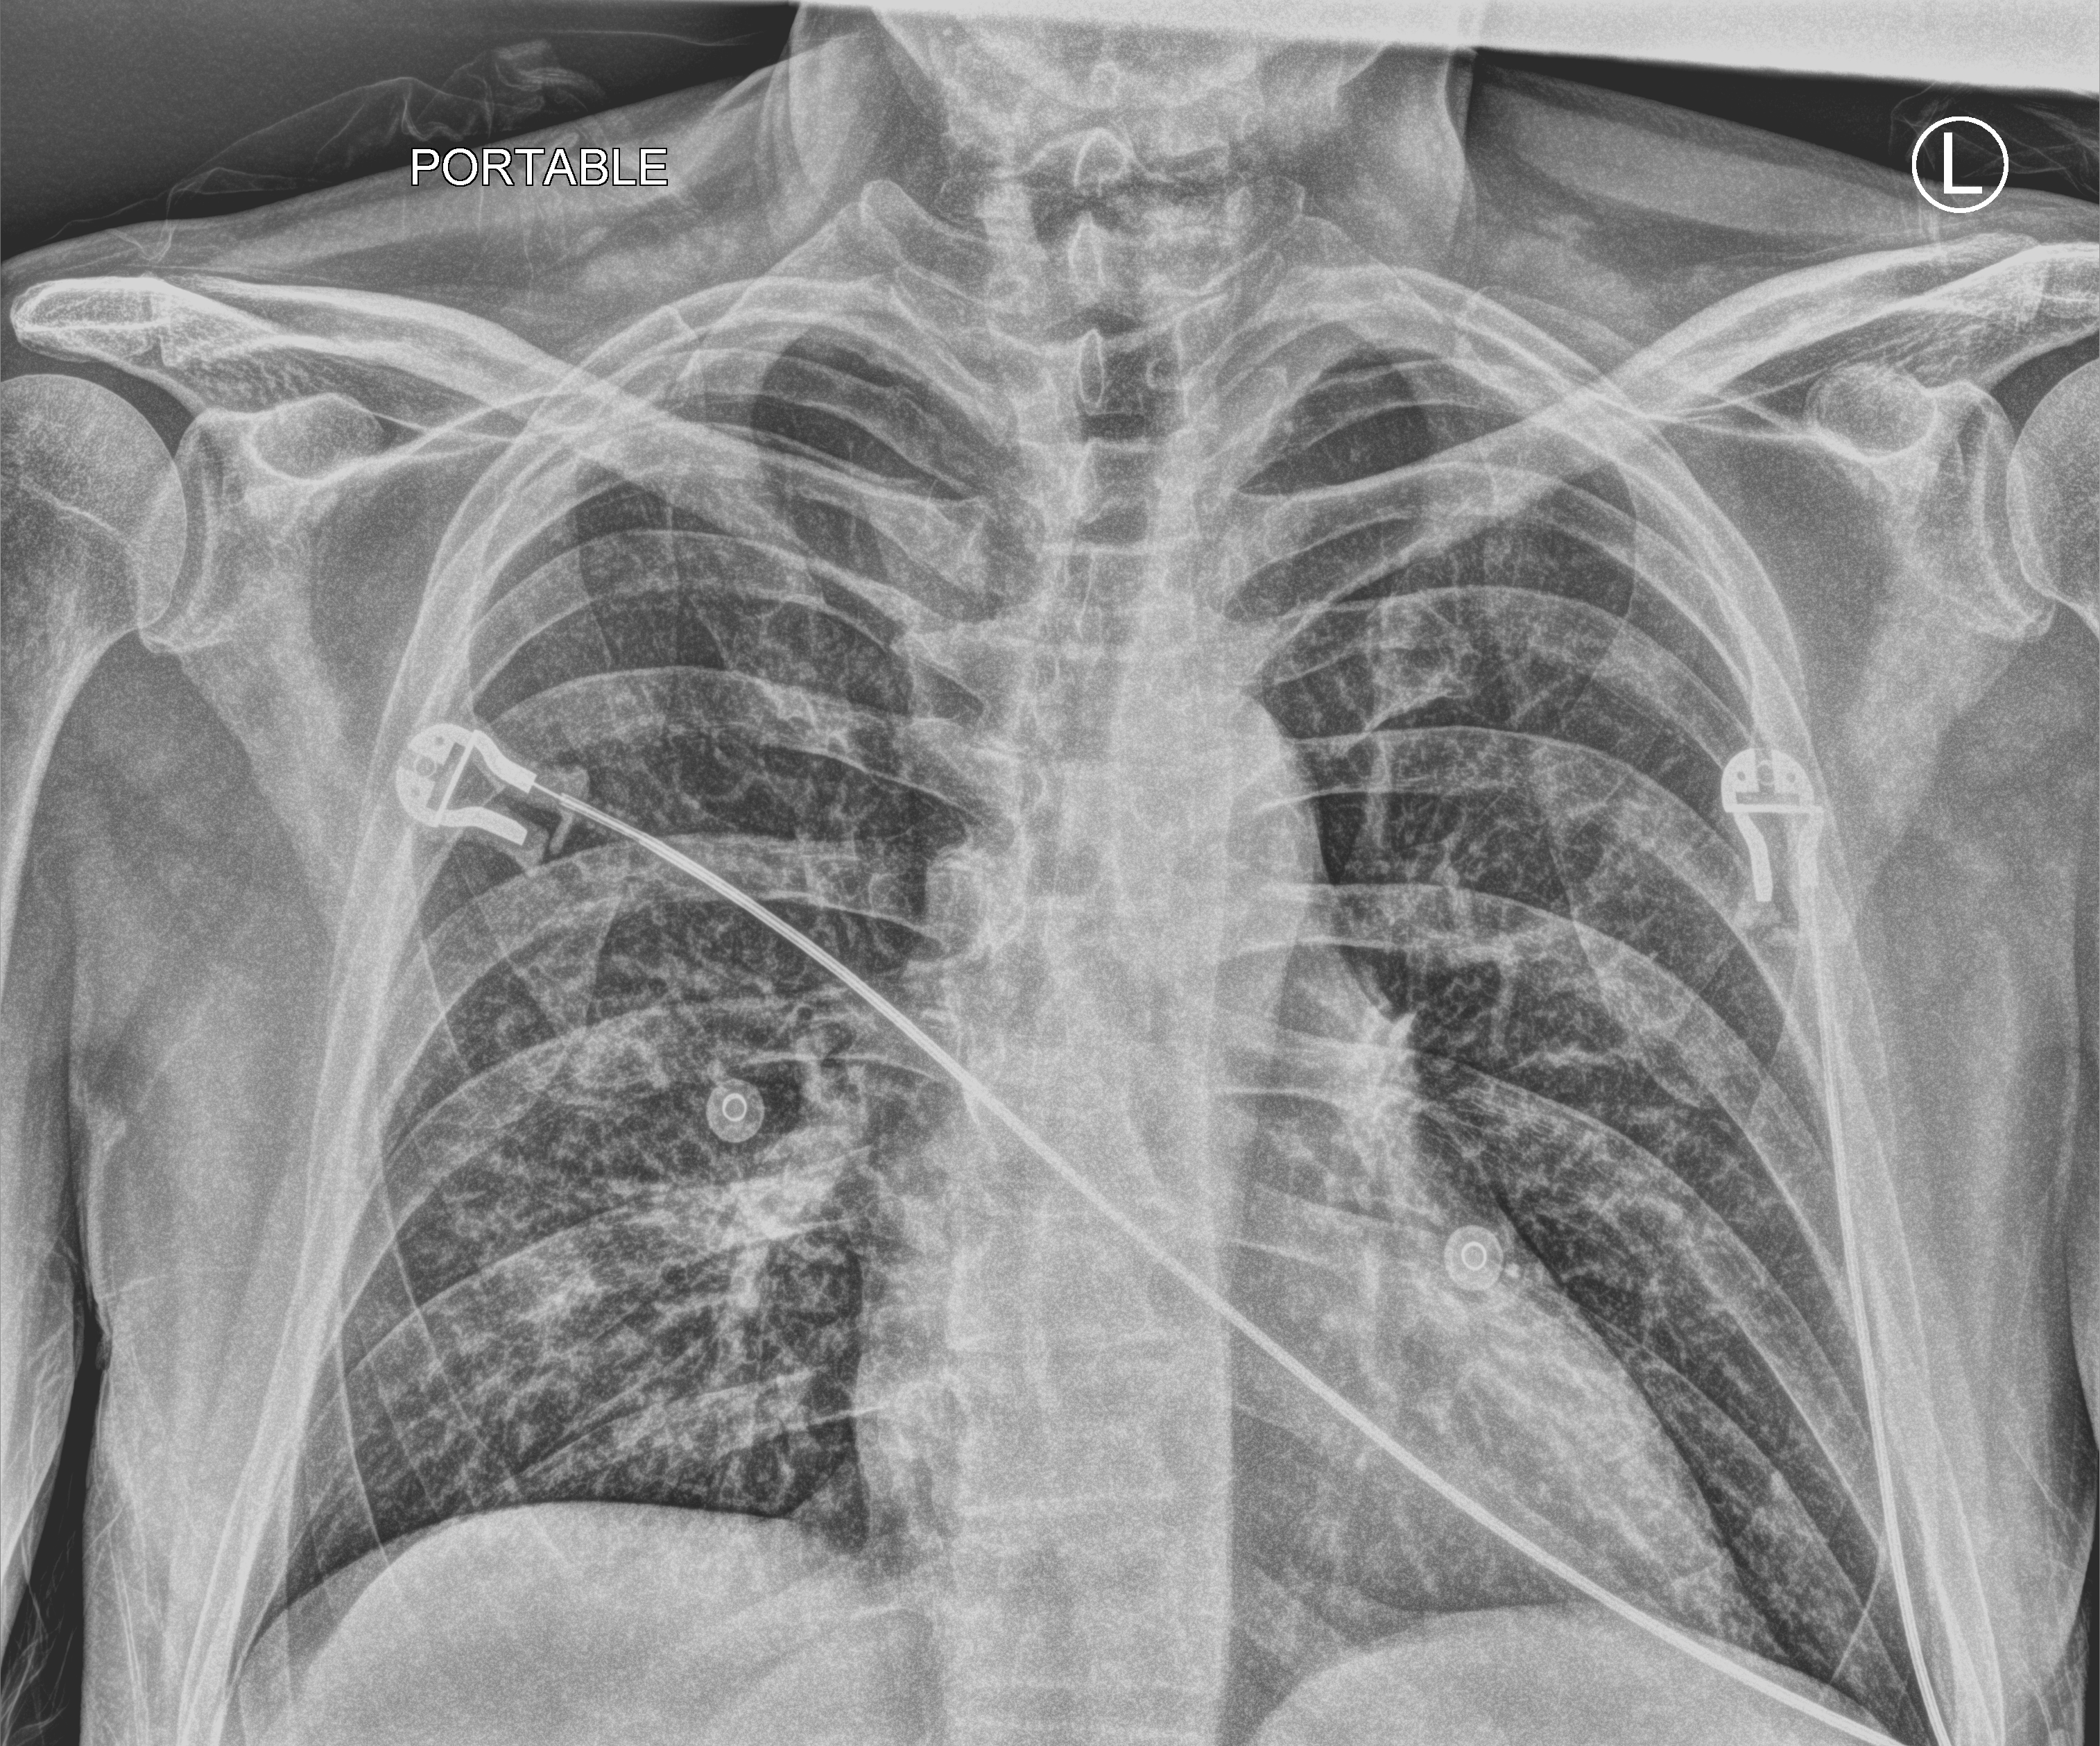
Portable chest radiograph; anteroposterior (AP) projection. Male patient hospitalised with COVID-19, age 60–74 years.
Hospital-stay facts (about this admission, not read from this image; timing relative to this image not recorded):
- admitted to intensive care during this hospital stay: no